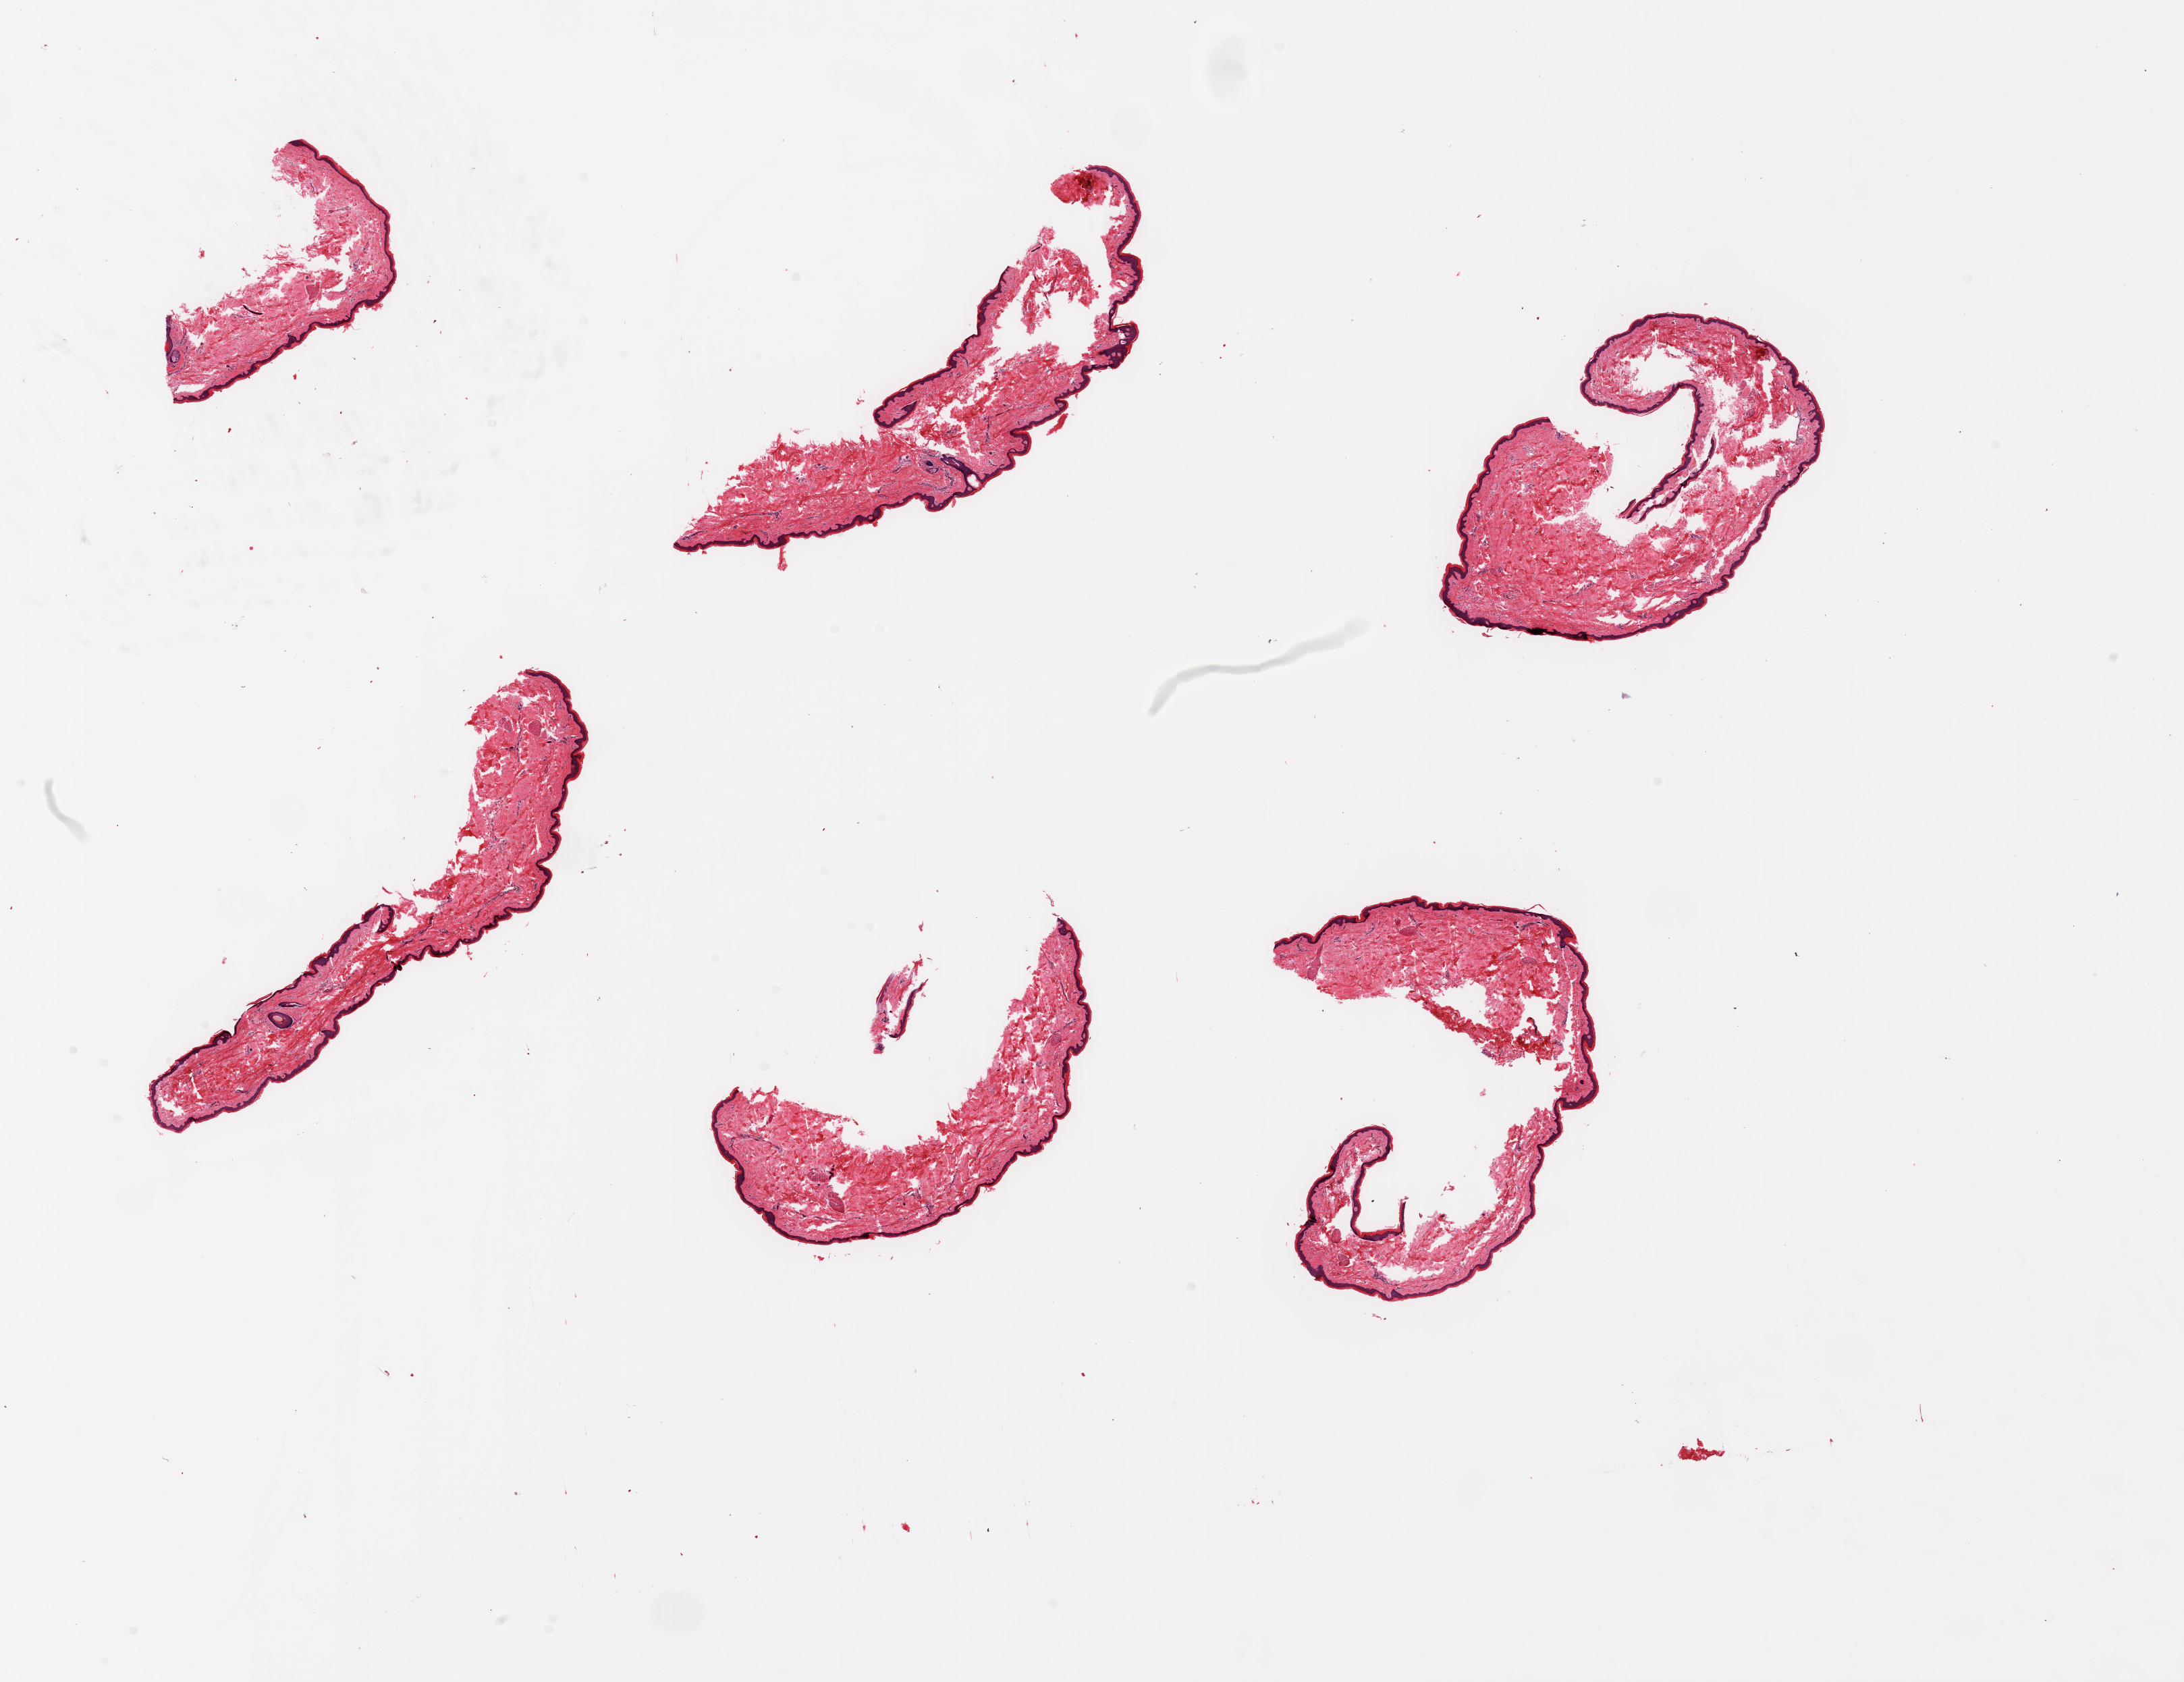
Whole-slide image, haematoxylin and eosin stain, shown as a low-resolution overview of the whole scanned area (about 25.6 x 19.7 mm, acquisition: 20x scan); PAXgene-fixed, paraffin-embedded tissue; section of skin of lower leg (target tissue); tissue donor sample.
* reviewer comment on this tissue sample: 6 pieces, squamous epithelium up to ~40 microns; no dermal fat